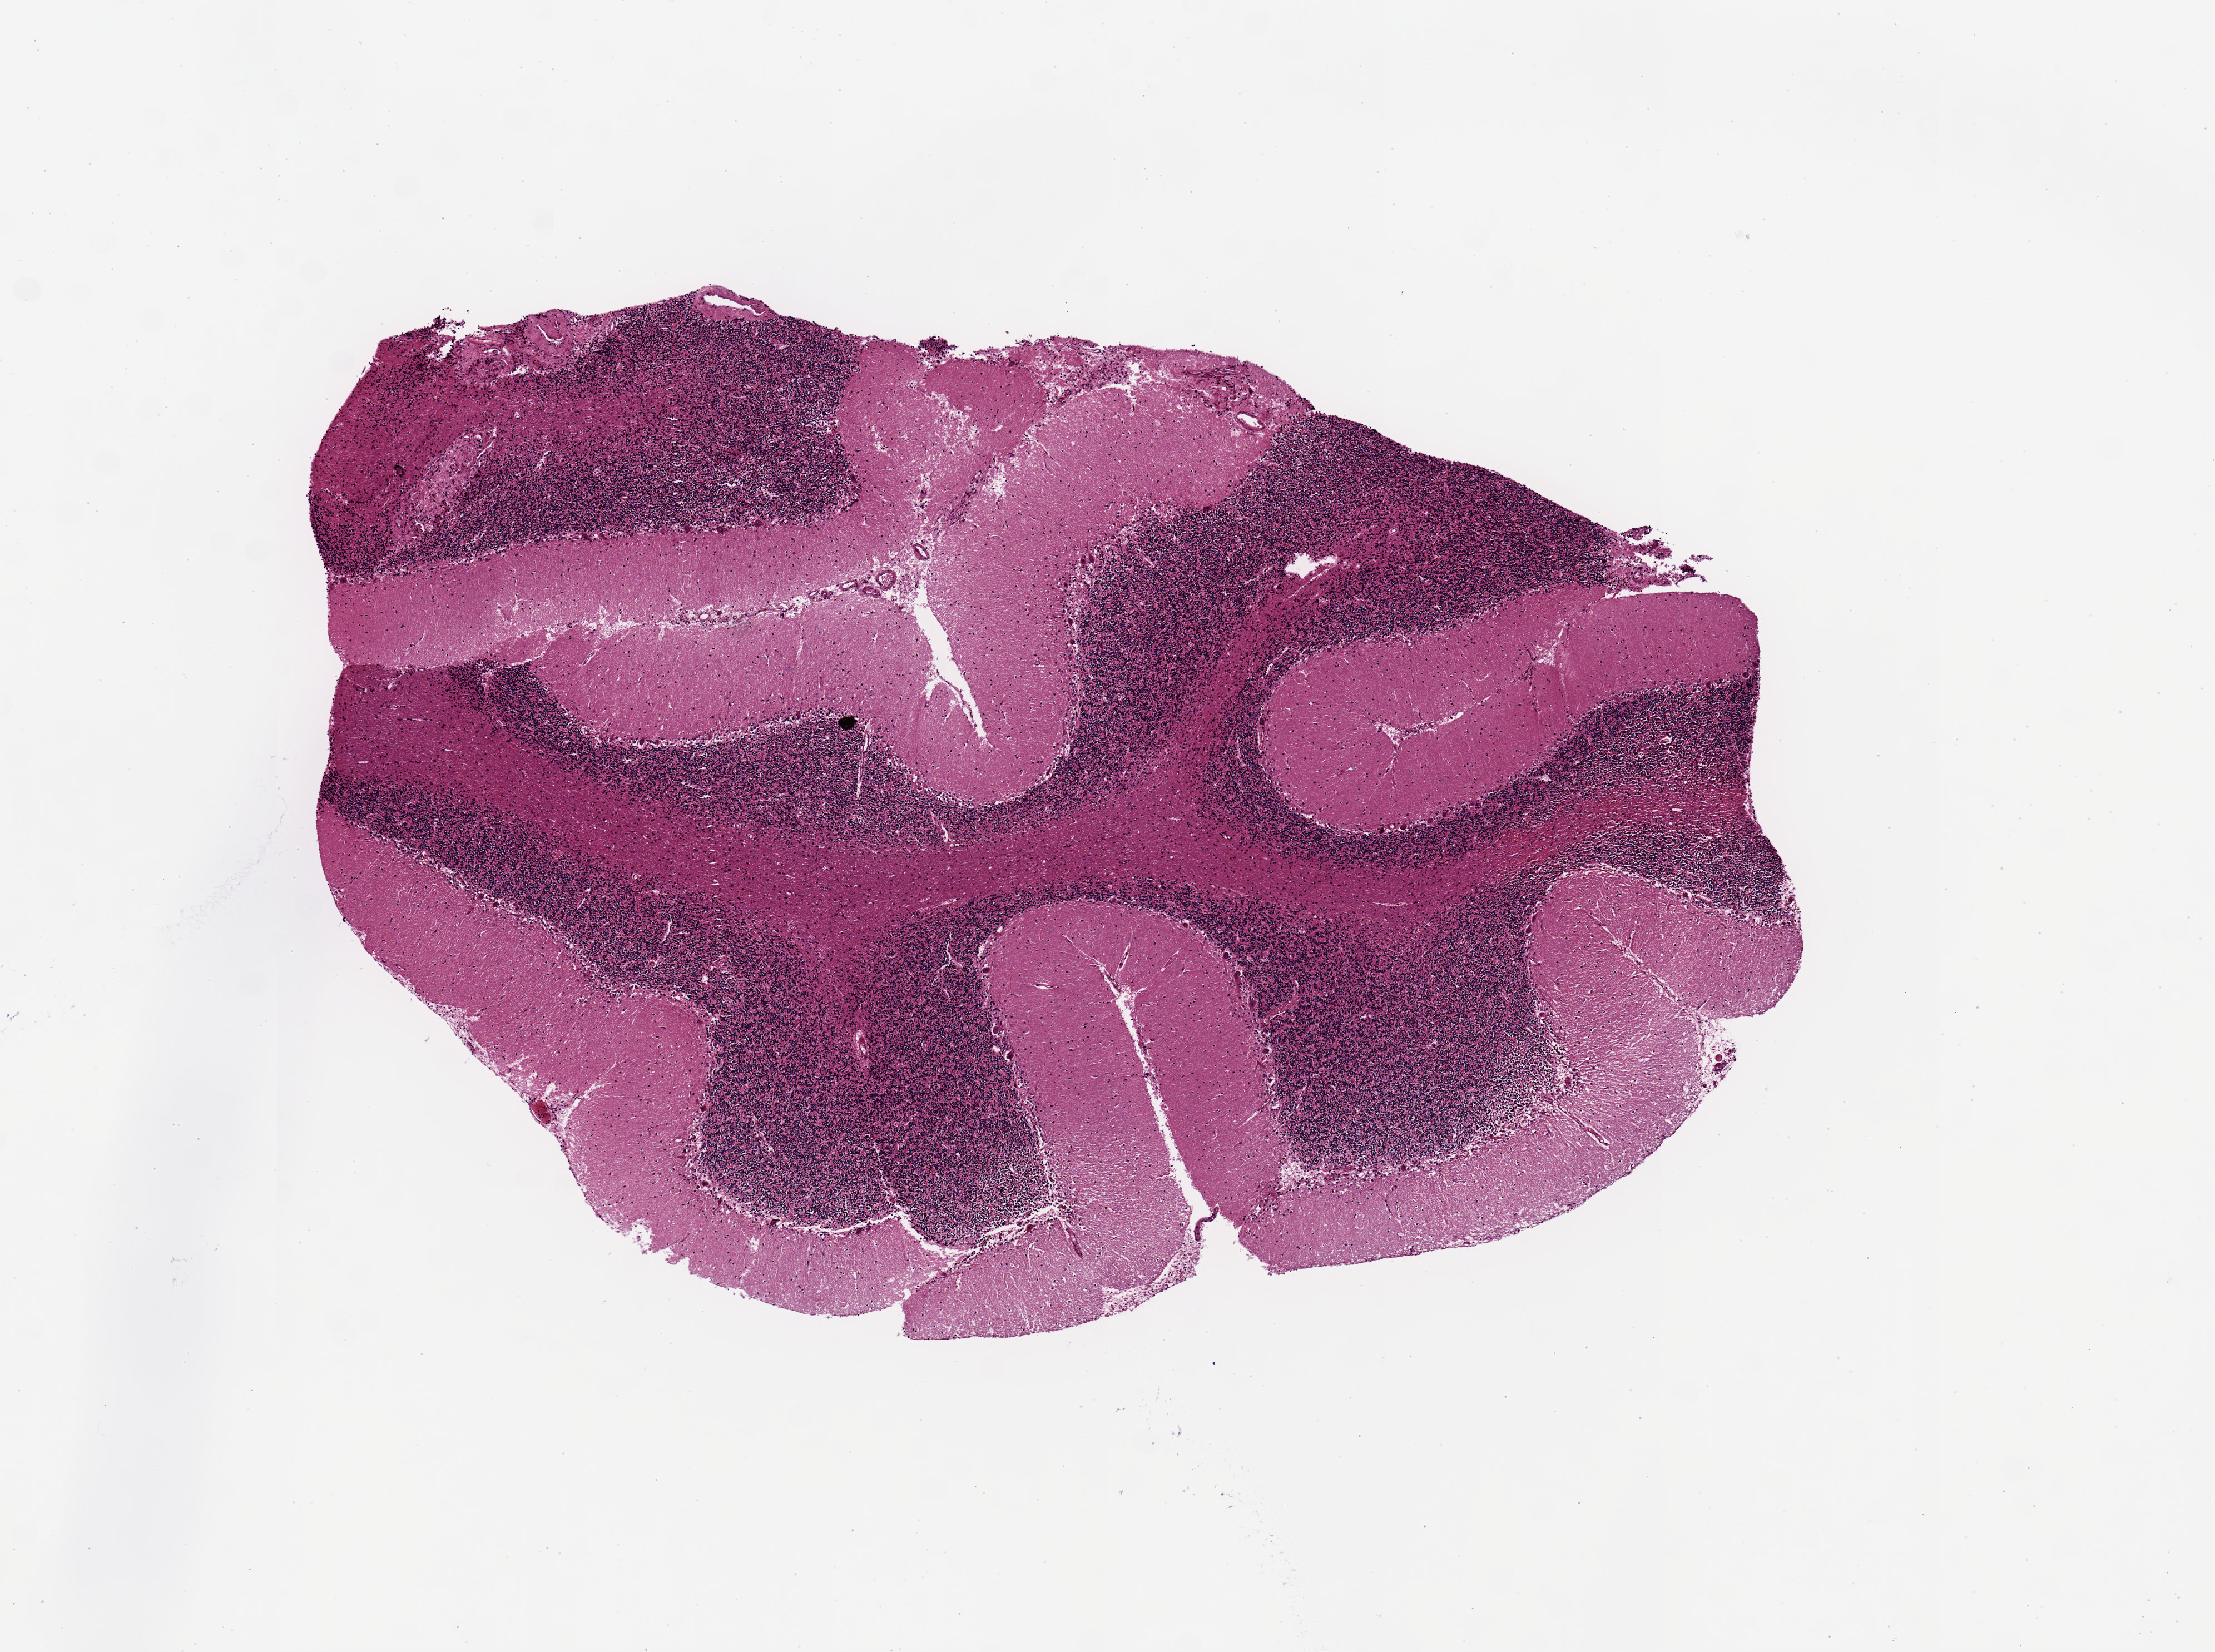
Digitized H&E-stained section, a low-resolution overview of the entire scanned area, about 7.9 x 5.9 mm. PAXgene-fixed paraffin-embedded (PFPE) section. Section of cerebellum (target tissue). Donor tissue sample.
* reviewer comment on this tissue sample: 5.4x3.7. Not cortex but cerebellum